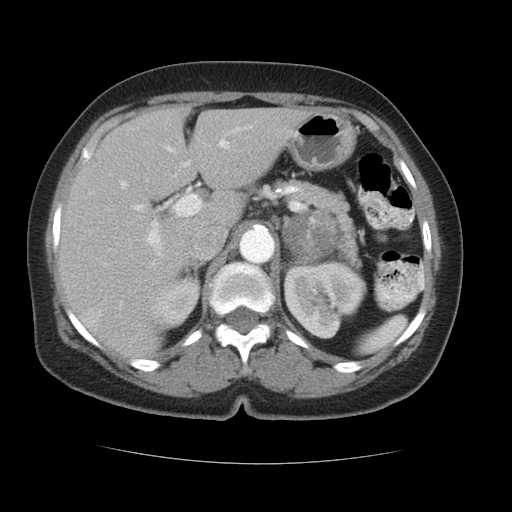
Contrast-enhanced abdominal CT, one axial slice; slice 68 of 96 in the series (ordered by position); reconstruction kernel STANDARD; 120 kVp; intravenous contrast given; soft-tissue window (W 400 / L 40 HU); 5 mm slice thickness; 512 × 512 image matrix, field of view 348 × 348 mm. Patient: female, 66 years. Case-level facts recorded for this patient, not image findings: diagnosis: adrenocortical carcinoma; tumour side: left adrenal; tumour size at pathology: 5.5 cm; Ki-67 index: 15 %; stage (as recorded): 3.
Outlined on this slice (semi-automatically segmented with operator editing):
- mass: bounding box [x1, y1, x2, y2] px = [284, 212, 339, 261]